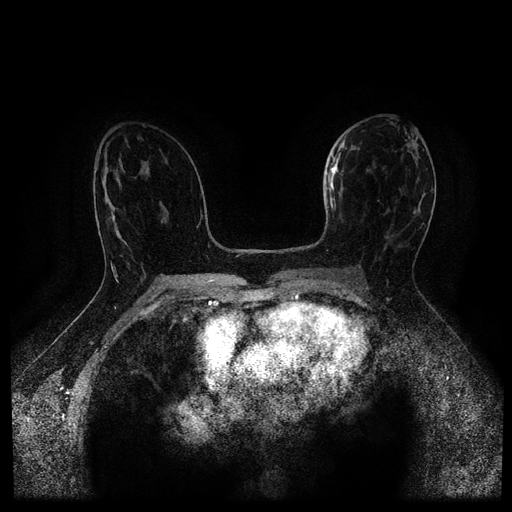
Breast MRI (dynamic contrast-enhanced, multi-phase), one axial slice. Slice 59 of 116 in the series (ordered by position). Dynamic contrast-enhanced series, time point 2 of 5 at this slice position (early post-contrast). 1.5 T. TE 2.7 ms, TR 5.4 ms. 2 mm slice thickness. 512 × 512 image matrix, field of view 340 × 340 mm. Patient: female, 50 years.
Structures marked on this image (semi-automatically segmented with operator editing):
- breast lesion (labelled 'tumour' in the annotation; benign lesions carry a separate 'benign' label): bounding box <326,147,341,212> (left, top, right, bottom; pixels)